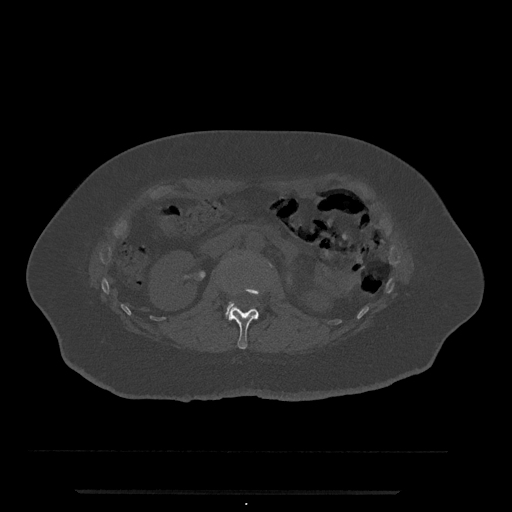
CT including the spine, one axial slice; position 78 of 797 along the scan axis; reconstruction kernel Br40s/3; bone window (W 1800 / L 400 HU); 0.5 mm slice thickness; 512 × 512 image matrix, field of view 440 × 440 mm. Patient: female, 51 years. From the clinical record (not read from this slice): primary cancer: neuro.
Annotated regions visible in this slice (semi-automatic segmentation, software-assisted and operator-edited):
- L1 vertebra: bounding box <226,287,262,349> (left, top, right, bottom; pixels)
- L2 vertebra: <227,302,238,313>